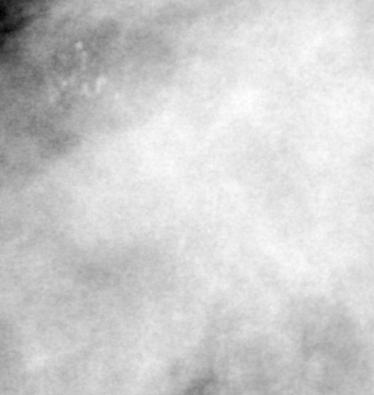
Region of interest cut from a scanned film mammogram (one marked finding), left breast, MLO view, BI-RADS breast density category 4 (scale 1–4).
Mass, shape irregular, margins ill defined; BI-RADS assessment category 4; pathology result (as recorded, not read from the image): malignant.